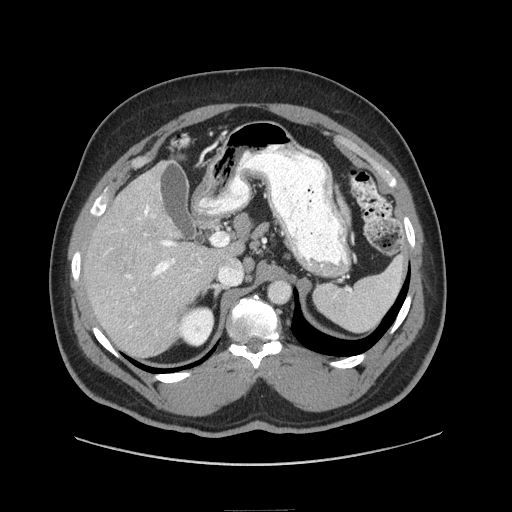
Contrast-enhanced abdominal CT (liver protocol), one axial slice. Position 47 of 87 along the scan axis. 140 kVp. Soft-tissue window (W 400 / L 40 HU). 2.5 mm slice thickness. 512 × 512 image matrix, field of view 440 × 440 mm. Case-level facts recorded for this patient, not image findings: diagnosis: hepatocellular carcinoma (patient treated with transarterial chemoembolisation; whether this scan precedes or follows treatment is not stated here); TNM stage (as recorded): Stage-II; Child-Pugh class: A.
Structures marked on this image (semi-automatically segmented with operator editing):
- liver parenchyma outside the tumour (the mass and vessels are separate outlines, so this box may not span the whole liver): bounding box <84,160,232,356> (left, top, right, bottom; pixels)
- liver vessels: <112,205,202,328>